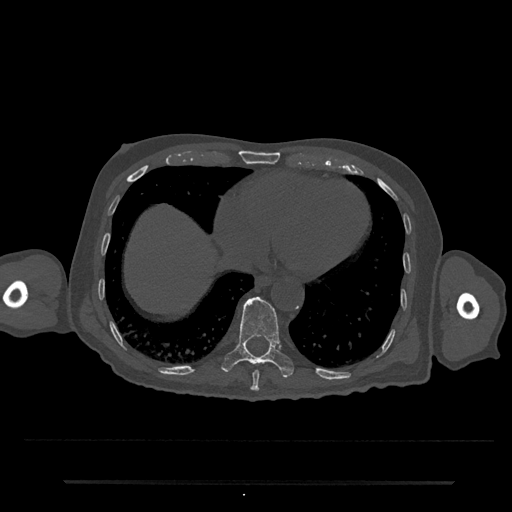
CT including the spine, one axial slice; slice 322 of 797 in the series (ordered by position); bone window (W 1800 / L 400 HU); 0.5 mm slice thickness; 512 × 512 image matrix. Male patient, age 74 years. From the clinical record (not read from this slice): primary cancer: prostate.
Annotated regions visible in this slice (semi-automatic segmentation, software-assisted and operator-edited):
- T10 vertebra: bounding box <222,296,294,378> (left, top, right, bottom; pixels)
- T9 vertebra: <250,370,259,391>